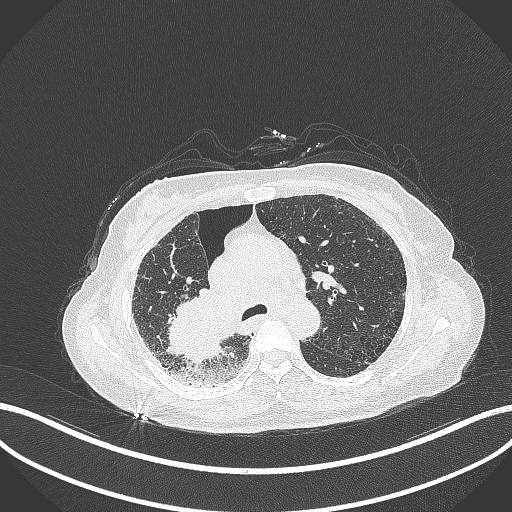
Chest CT, one axial slice. Position 228 of 408 along the scan axis. 120 kVp. Lung window (W 1500 / L -600 HU). 512 × 512 image matrix. Patient: female, 64 years. From the clinical record (not read from this slice): clinical TNM (as recorded): T3 N3 M0.
Annotated regions visible in this slice (rectangle marked by the reading radiologist):
- lung tumour (recorded histology: squamous cell carcinoma): box from (x=164, y=286) to (x=230, y=368) px